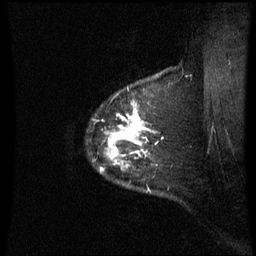
Breast MRI (dynamic contrast-enhanced), one sagittal slice; slice 54 of 60 in the series (ordered by position); dynamic contrast-enhanced series, image 2 of 3 at this slice position (ordered by acquisition); 1.5 T; TE 4.2 ms, TR 8.9 ms; 2.4 mm slice thickness; 256 × 256 image matrix, field of view 210 × 210 mm. Patient: female, 42 years. Case-level facts recorded for this patient, not image findings: setting: breast cancer imaged before/during neoadjuvant chemotherapy; receptor status: HER2-positive.
Outlined on this slice (semi-automatically segmented with operator editing):
- analysis volume of interest (the breast-tissue region the enhancement analysis was run in; not a lesion): bounding box (x1, y1, x2, y2) in pixels: (96, 103, 165, 191)
- tumour enhancement mask (voxels above the 70 % enhancement threshold inside the analysis volume of interest): (110, 109, 148, 158)